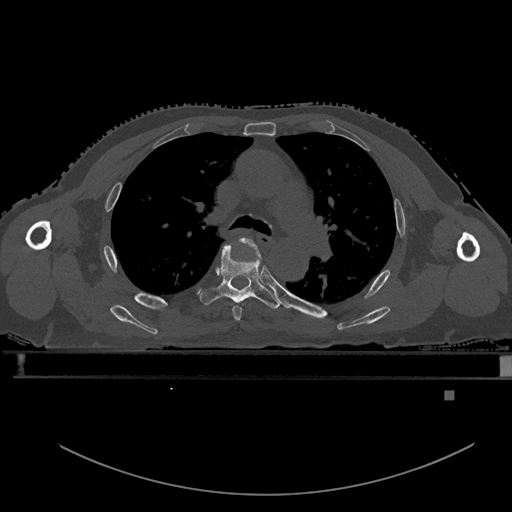
CT including the spine, one axial slice; bone window (W 1800 / L 400 HU); 0.5 mm slice thickness; 512 × 512 image matrix, field of view 456 × 456 mm. Male patient, age 82 years. Case-level facts recorded for this patient, not image findings: primary cancer: prostate; vertebrae with lytic lesions (as recorded): T11, T9, T8, T2.
Structures marked on this image (semi-automatic segmentation, software-assisted and operator-edited):
- T4 vertebra: box from (x=233, y=238) to (x=261, y=321) px
- T5 vertebra: (x=200, y=244)–(x=280, y=309)